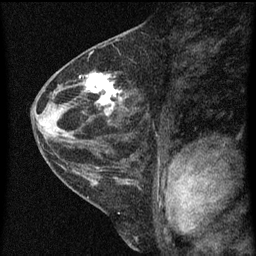
Breast MRI (dynamic contrast-enhanced), one sagittal slice; slice 29 of 60 in the series (ordered by position); dynamic contrast-enhanced series, image 2 of 3 at this slice position (ordered by acquisition); 1.5 T; TE 4.2 ms, TR 8 ms; 2 mm slice thickness; 256 × 256 image matrix, field of view 180 × 180 mm. Patient: female, 48 years.
Structures marked on this image (semi-automatically segmented with operator editing):
- analysis volume of interest (the breast-tissue region the enhancement analysis was run in; not a lesion): bounding box (x1, y1, x2, y2) in pixels: (82, 68, 126, 125)
- tumour enhancement mask (voxels above the 70 % enhancement threshold inside the analysis volume of interest): (86, 74, 123, 117)